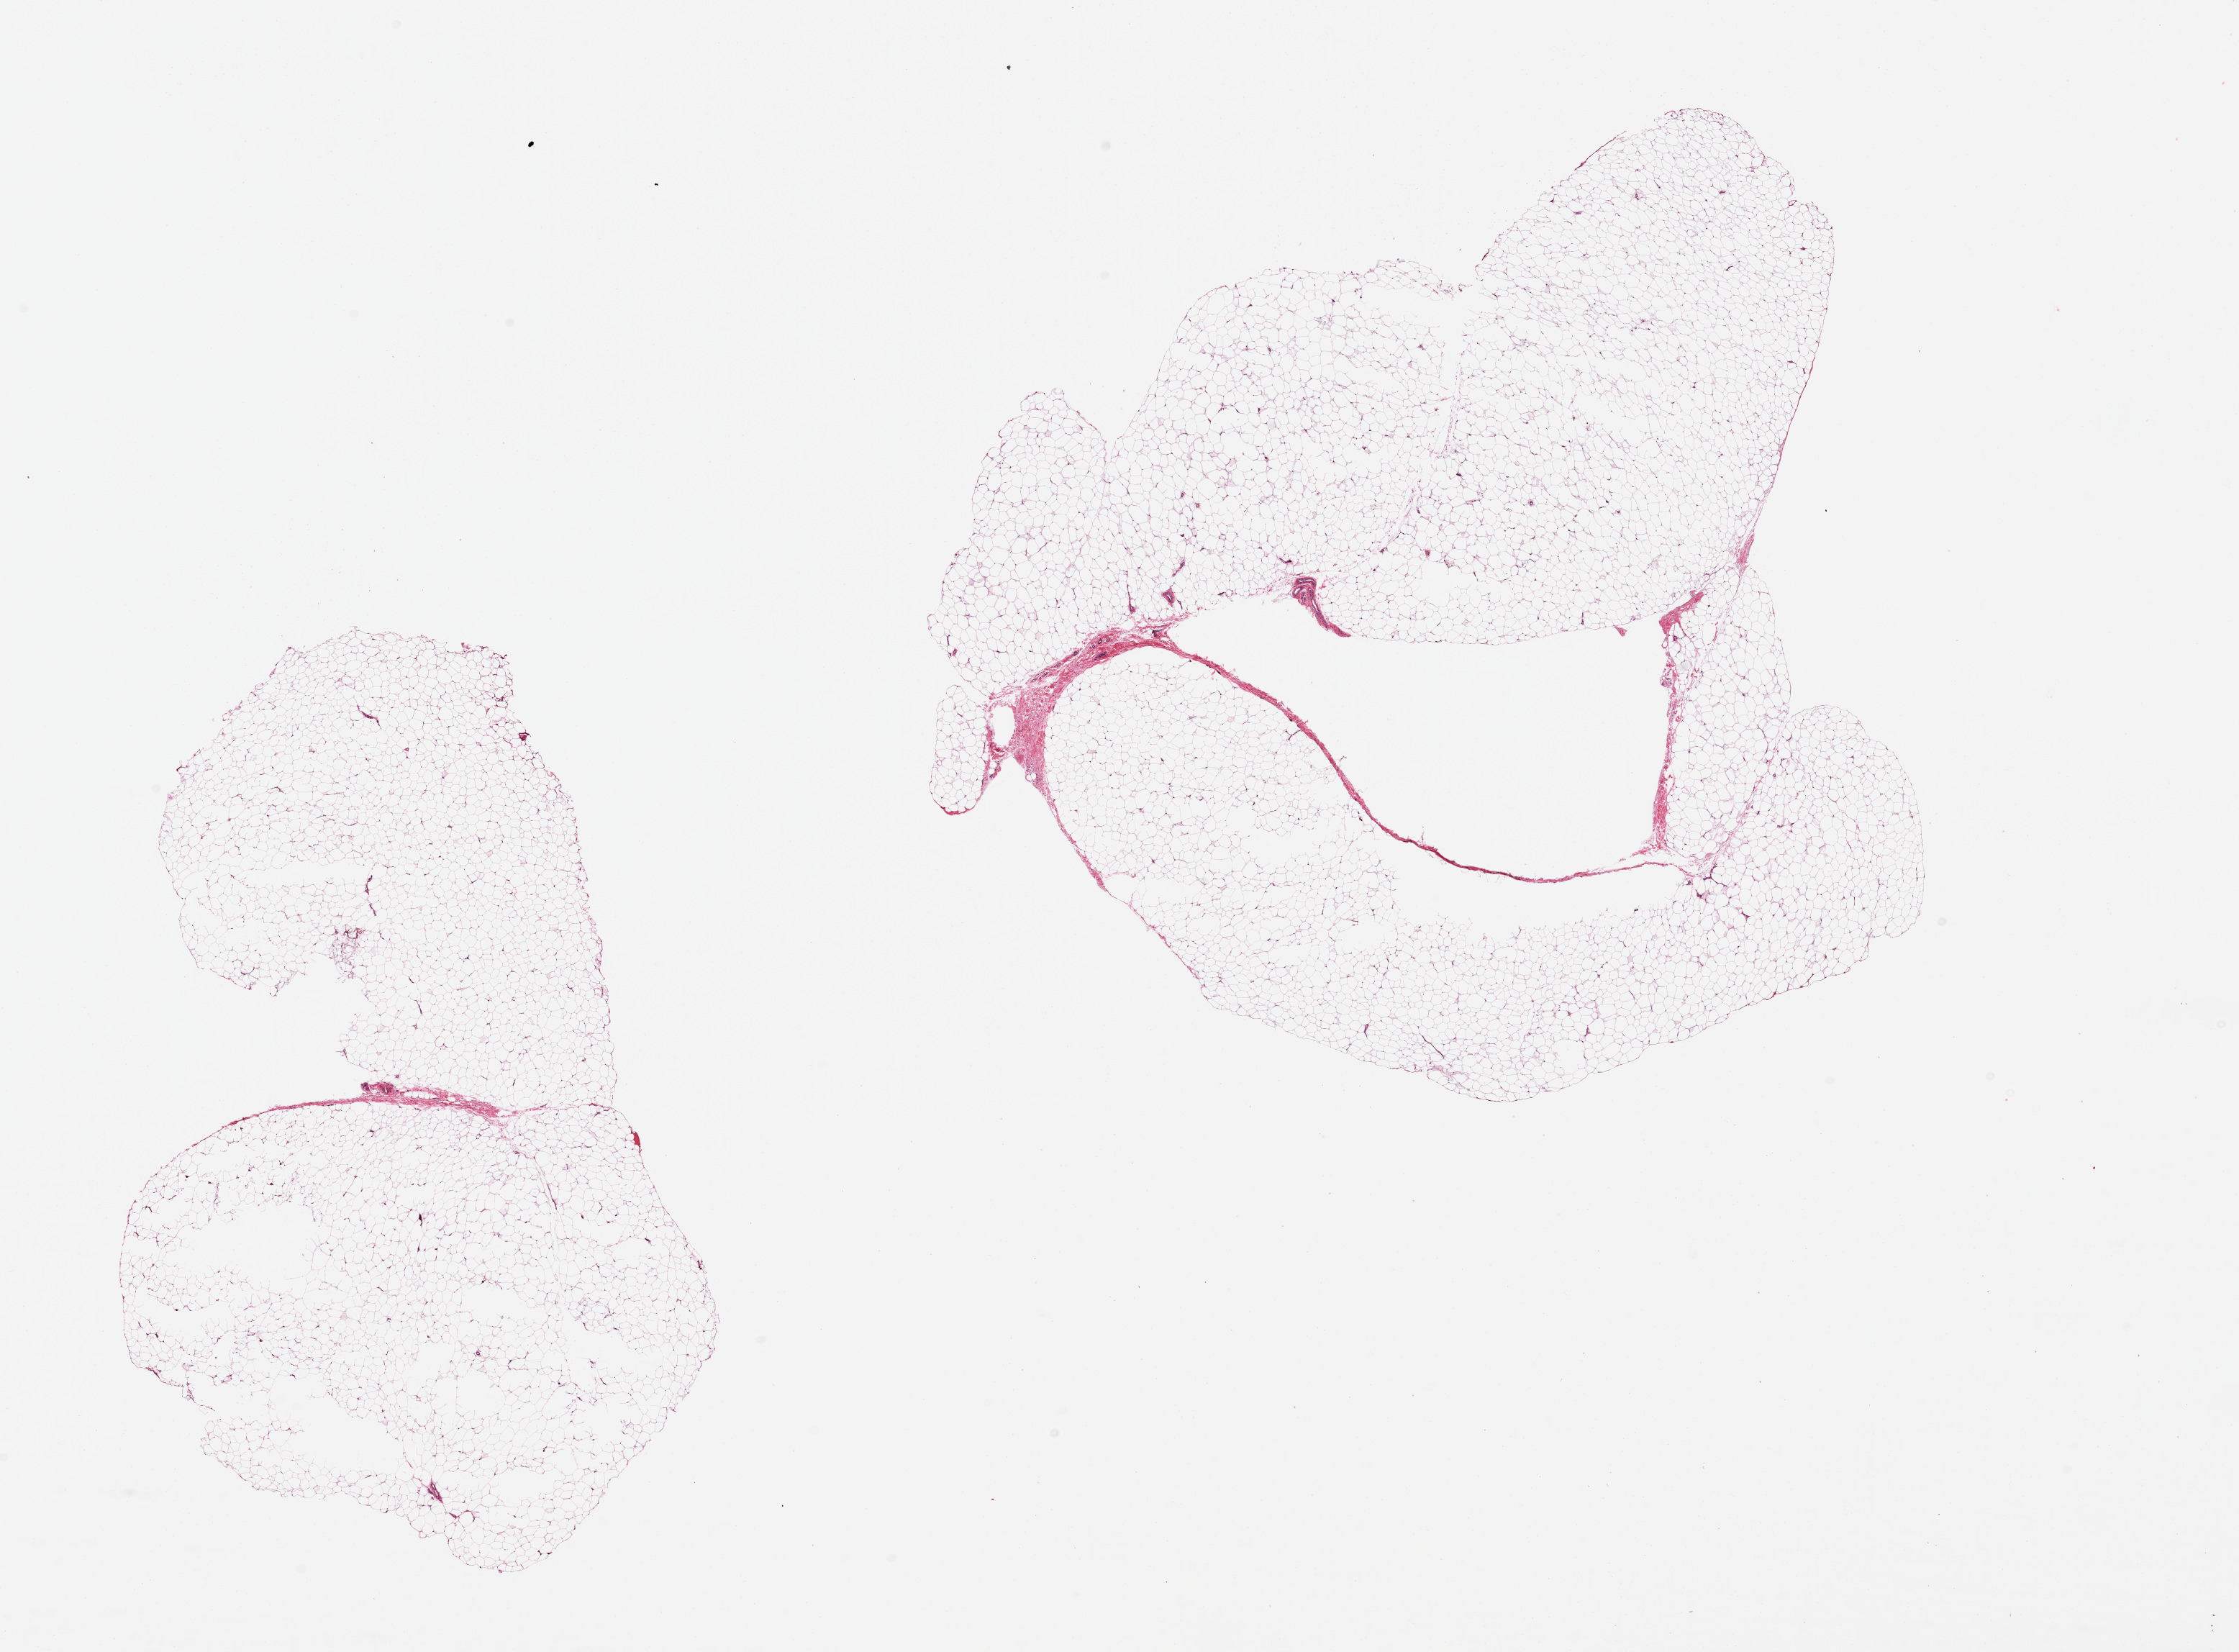
Whole-slide image, H&E stain, shown as a low-resolution overview of the whole scanned area (about 24.6 x 18.2 mm); PAXgene-fixed, paraffin-embedded tissue; target tissue: adipose tissue; tissue donor sample. Donor sex: female.
Pathologist's review note for this sample: 2 pieces; mature adipose tissue.